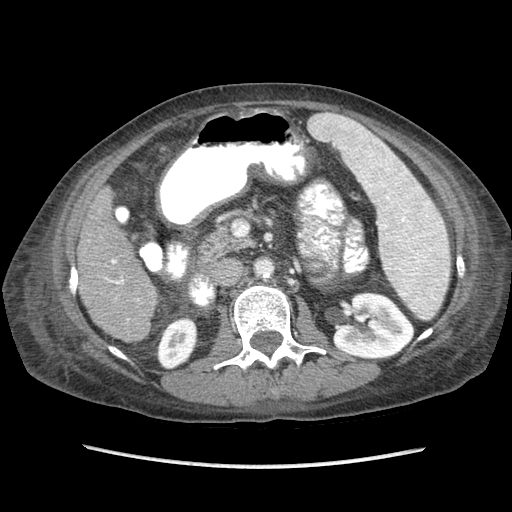
Contrast-enhanced abdominal CT (liver protocol), one axial slice; position 29 of 87 along the scan axis; reconstruction kernel STANDARD; soft-tissue window (W 400 / L 40 HU); 2.5 mm slice thickness; 512 × 512 image matrix. From the clinical record (not read from this slice): diagnosis: hepatocellular carcinoma (patient treated with transarterial chemoembolisation; whether this scan precedes or follows treatment is not stated here); TNM stage (as recorded): Stage-IIIB; Child-Pugh class: A; tumour differentiation: no biopsy.
Annotated regions visible in this slice (semi-automatic segmentation, software-assisted and operator-edited):
- liver parenchyma outside the tumour (the mass and vessels are separate outlines, so this box may not span the whole liver): bounding box (x1, y1, x2, y2) in pixels: (78, 188, 158, 342)
- liver vessels: (106, 259, 139, 320)